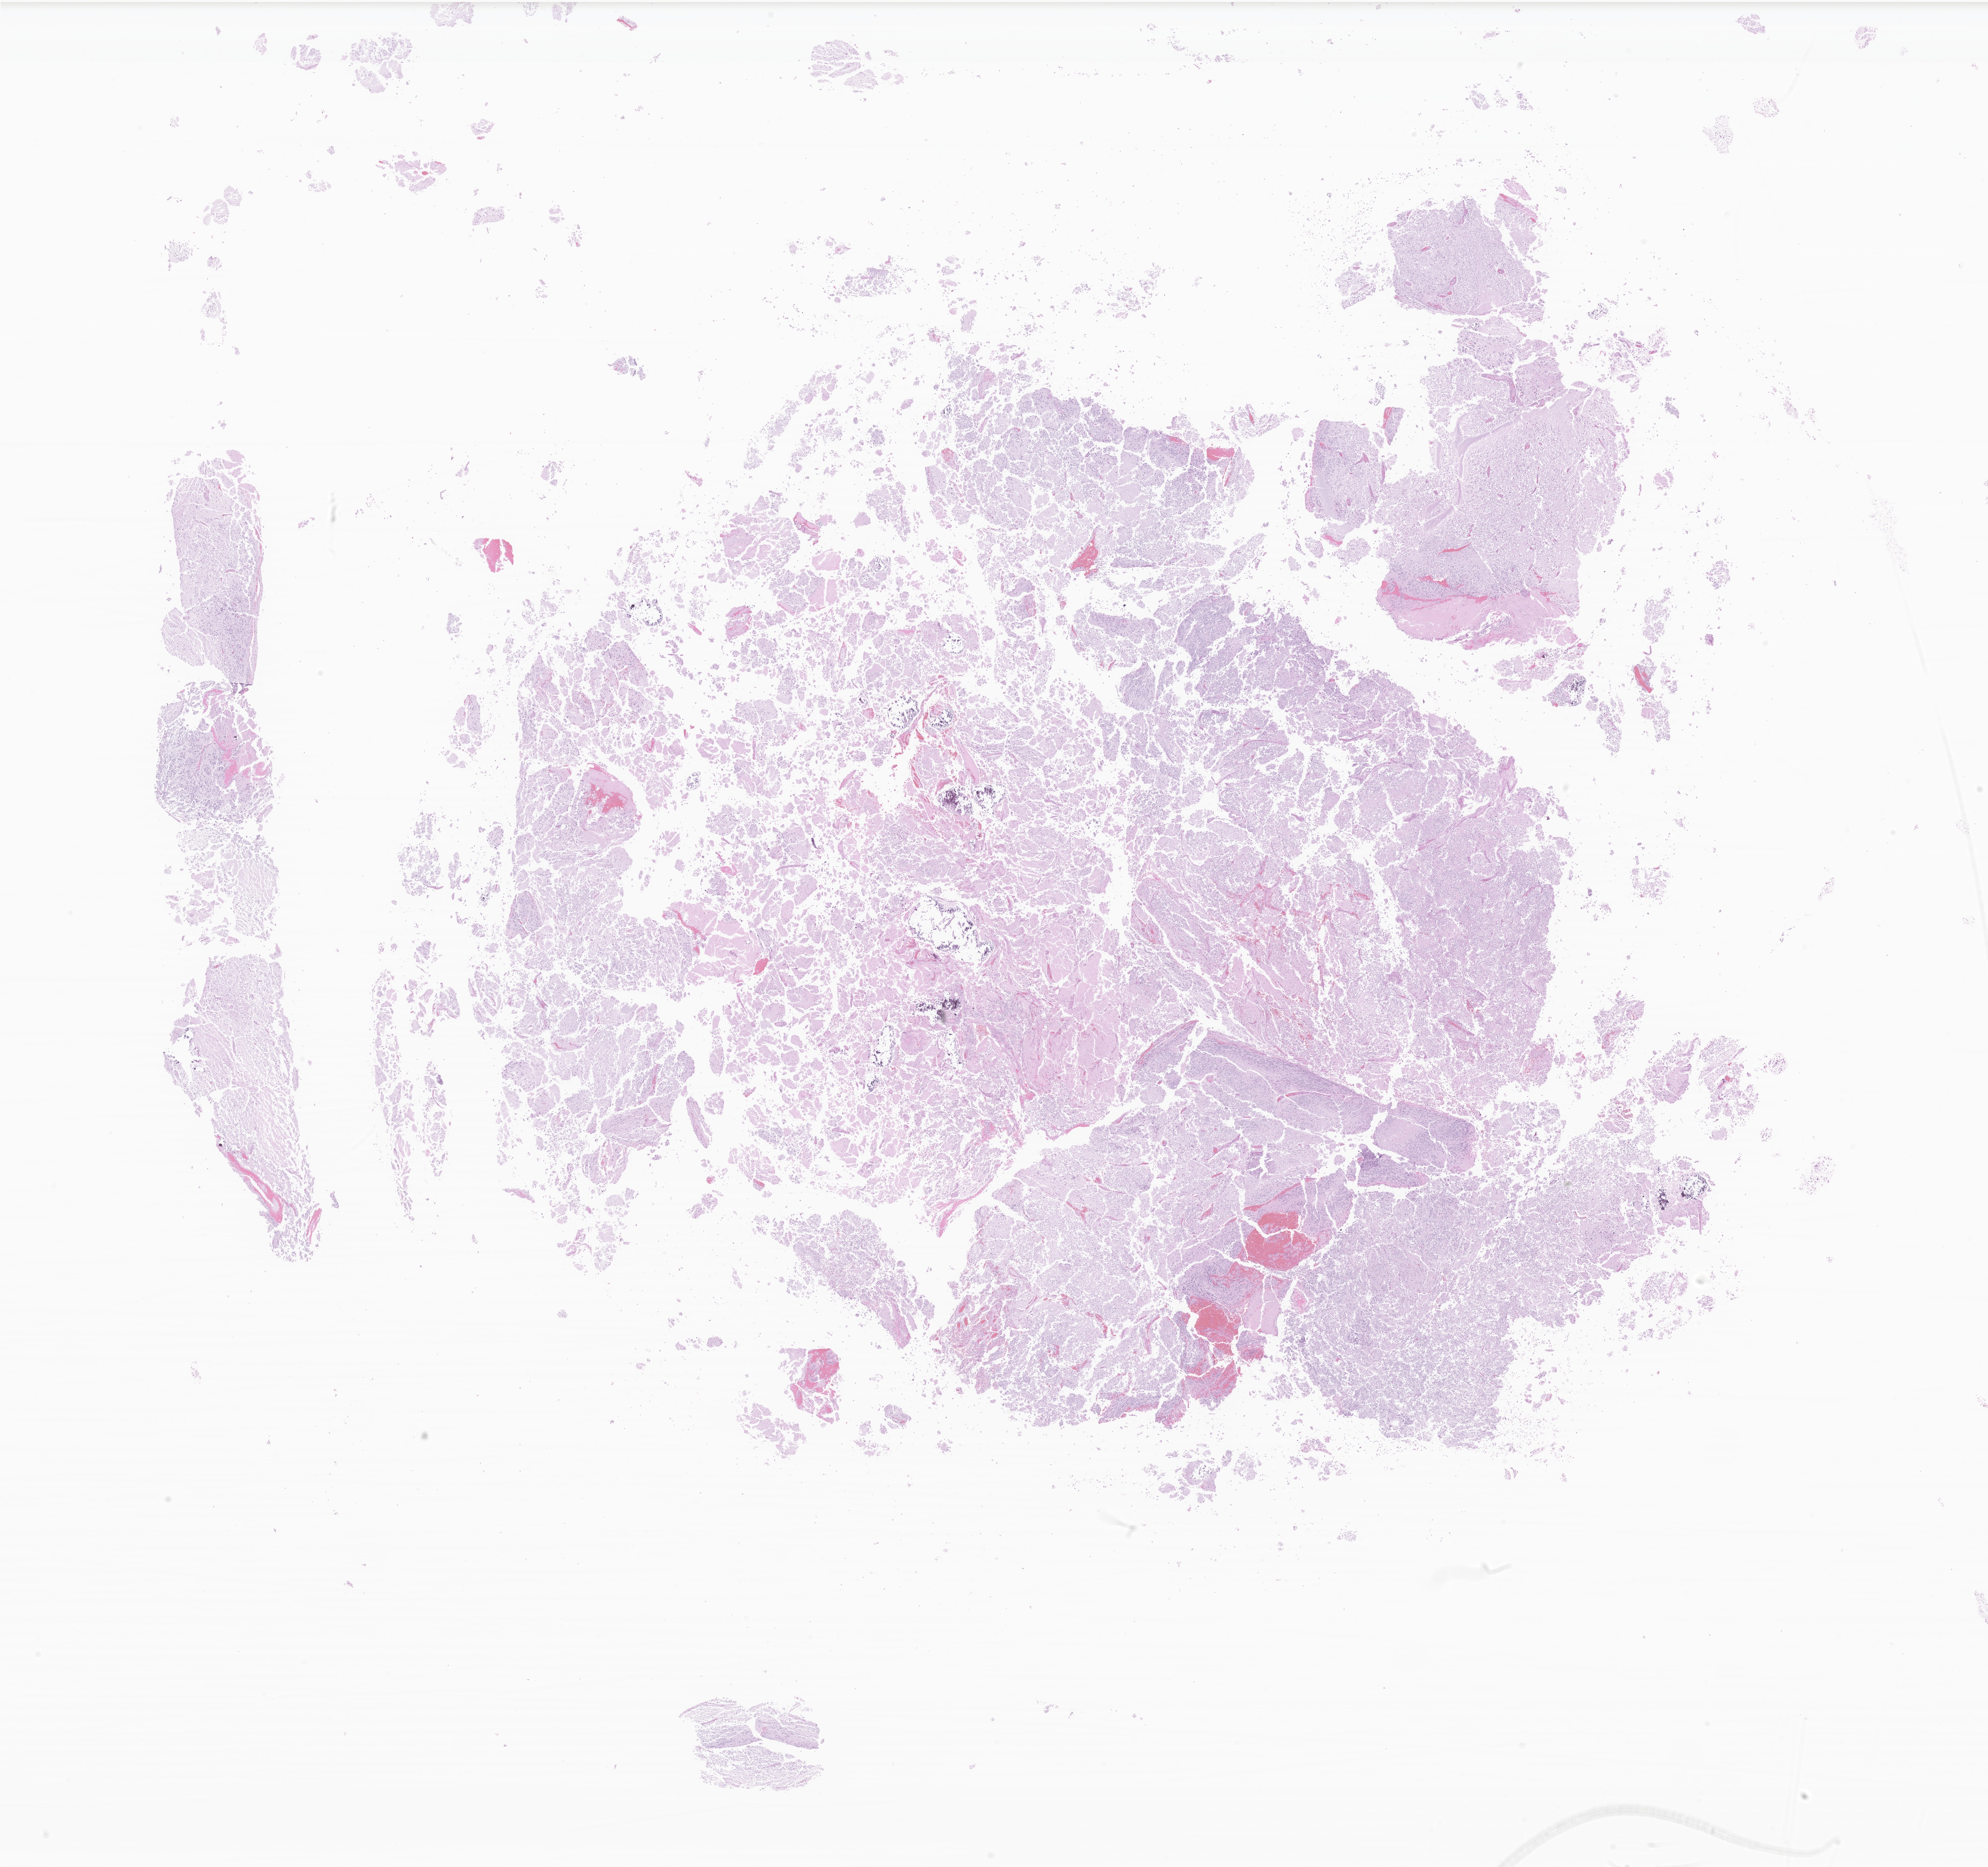
Digitized haematoxylin and eosin-stained section of tumor tissue from the frontal lobe, whole scanned area (about 24.7 x 23.2 mm) shown as a low-resolution overview. Formalin-fixed paraffin-embedded section. Patient female; age 97 months (8 years 1 month).
Diagnosis: Neoplasm, uncertain whether benign or malignant.